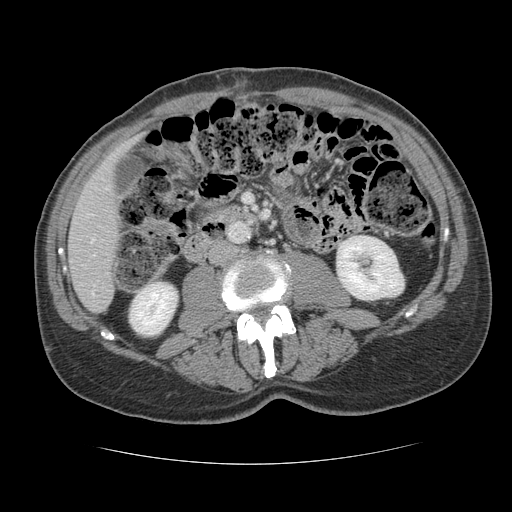
Contrast-enhanced abdominal CT, one axial slice. 120 kVp. Intravenous contrast given. Soft-tissue window (W 400 / L 40 HU). 512 × 512 image matrix, field of view 377 × 377 mm. Male patient, age 68 years. Case-level facts recorded for this patient, not image findings: diagnosis: colorectal cancer liver metastases, imaged before liver resection; multiple liver metastases: yes; largest metastasis: 2.2 cm.
Outlined on this slice (expert manual segmentation):
- hepatic veins: bounding box <91,238,94,242> (left, top, right, bottom; pixels)
- liver: <69,162,121,312>
- planned liver remnant (the part of the liver to remain after resection): <69,160,121,312>
- portal vein (with intrahepatic branches): <92,292,94,294>